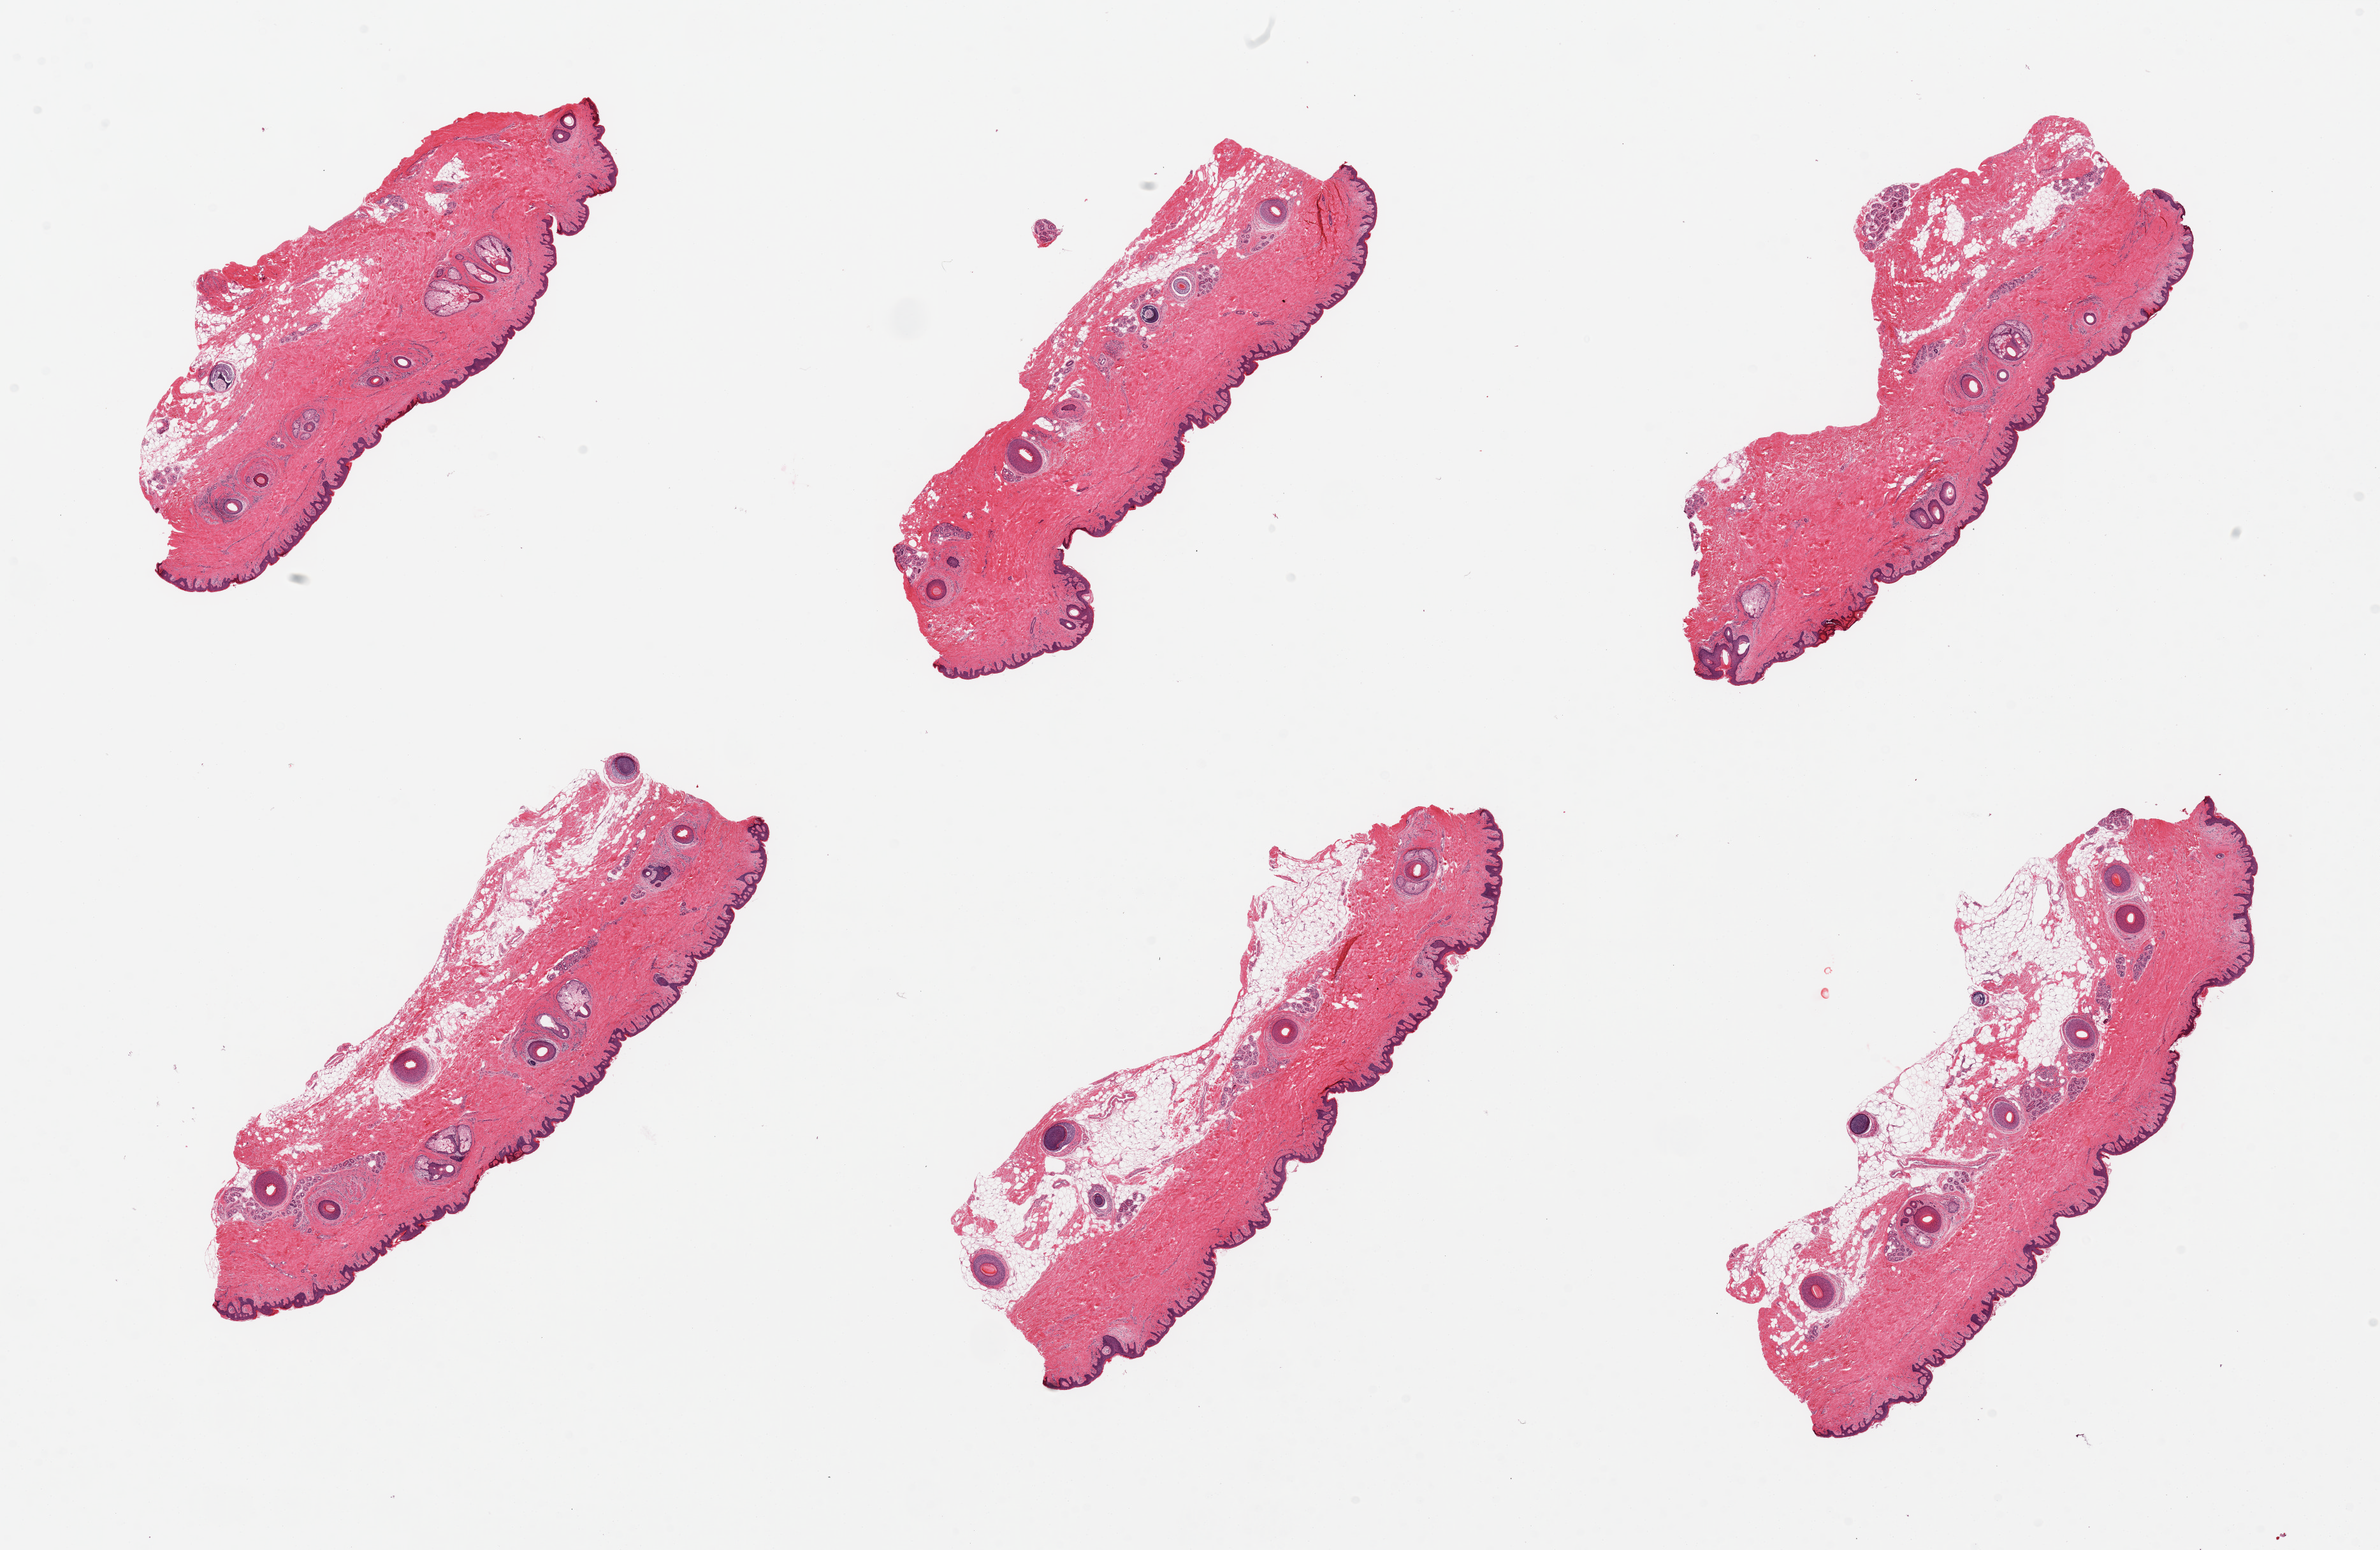
Digitized hematoxylin and eosin (H&E)-stained section, brightfield — shown as a low-resolution overview of the whole scanned area (about 29.5 x 19.2 mm); PAXgene-fixed, paraffin-embedded tissue; section of skin of suprapubic region (target tissue); tissue donor sample. Donor: male.
Review note (as recorded): 6 pieces; all are hair-bearing [not target]; up to 1 mm subcutaneous fat.